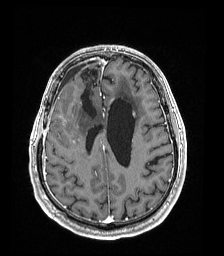
Brain MRI from a brain-tumour surgery series, one axial slice; position 64 of 192 along the scan axis; T1-weighted post-contrast; 1 mm slice thickness; 224 × 256 image matrix, field of view 224 × 256 mm. Case-level facts recorded for this patient, not image findings: histopathology: Astrocytoma; WHO grade: 4; IDH mutation: yes; tumour location: Right Frontal.
Annotated regions visible in this slice (outlined manually by an expert reader):
- previous resection cavity: box from (x=81, y=67) to (x=98, y=117) px
- tumour: (x=72, y=140)–(x=76, y=145)